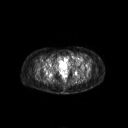
FDG PET of an extremity soft-tissue mass (from a PET/CT study), one axial slice; slice 54 of 267 in the series (ordered by position); 3.27 mm slice thickness; 128 × 128 image matrix. Patient: female, 47 years. From the clinical record (not read from this slice): histological type: myxofibrosarcoma; grade: intermediate; site of the primary tumour: left thigh.
Structures marked on this image (expert contour drawn on MRI and transferred to this co-registered scan by the dataset authors):
- gross tumour volume including surrounding oedema: bounding box (x1, y1, x2, y2) in pixels: (66, 57, 82, 63)